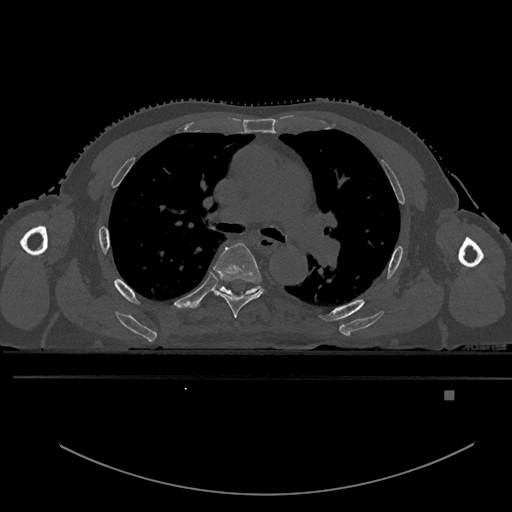
CT including the spine, one axial slice; slice 345 of 969 in the series (ordered by position); bone window (W 1800 / L 400 HU); 512 × 512 image matrix, field of view 456 × 456 mm. Male patient, age 82 years. Case-level facts recorded for this patient, not image findings: primary cancer: prostate.
Annotated regions visible in this slice (semi-automatic segmentation, software-assisted and operator-edited):
- T5 vertebra: bounding box (x1, y1, x2, y2) in pixels: (213, 242, 263, 318)
- T6 vertebra: (216, 285, 261, 297)